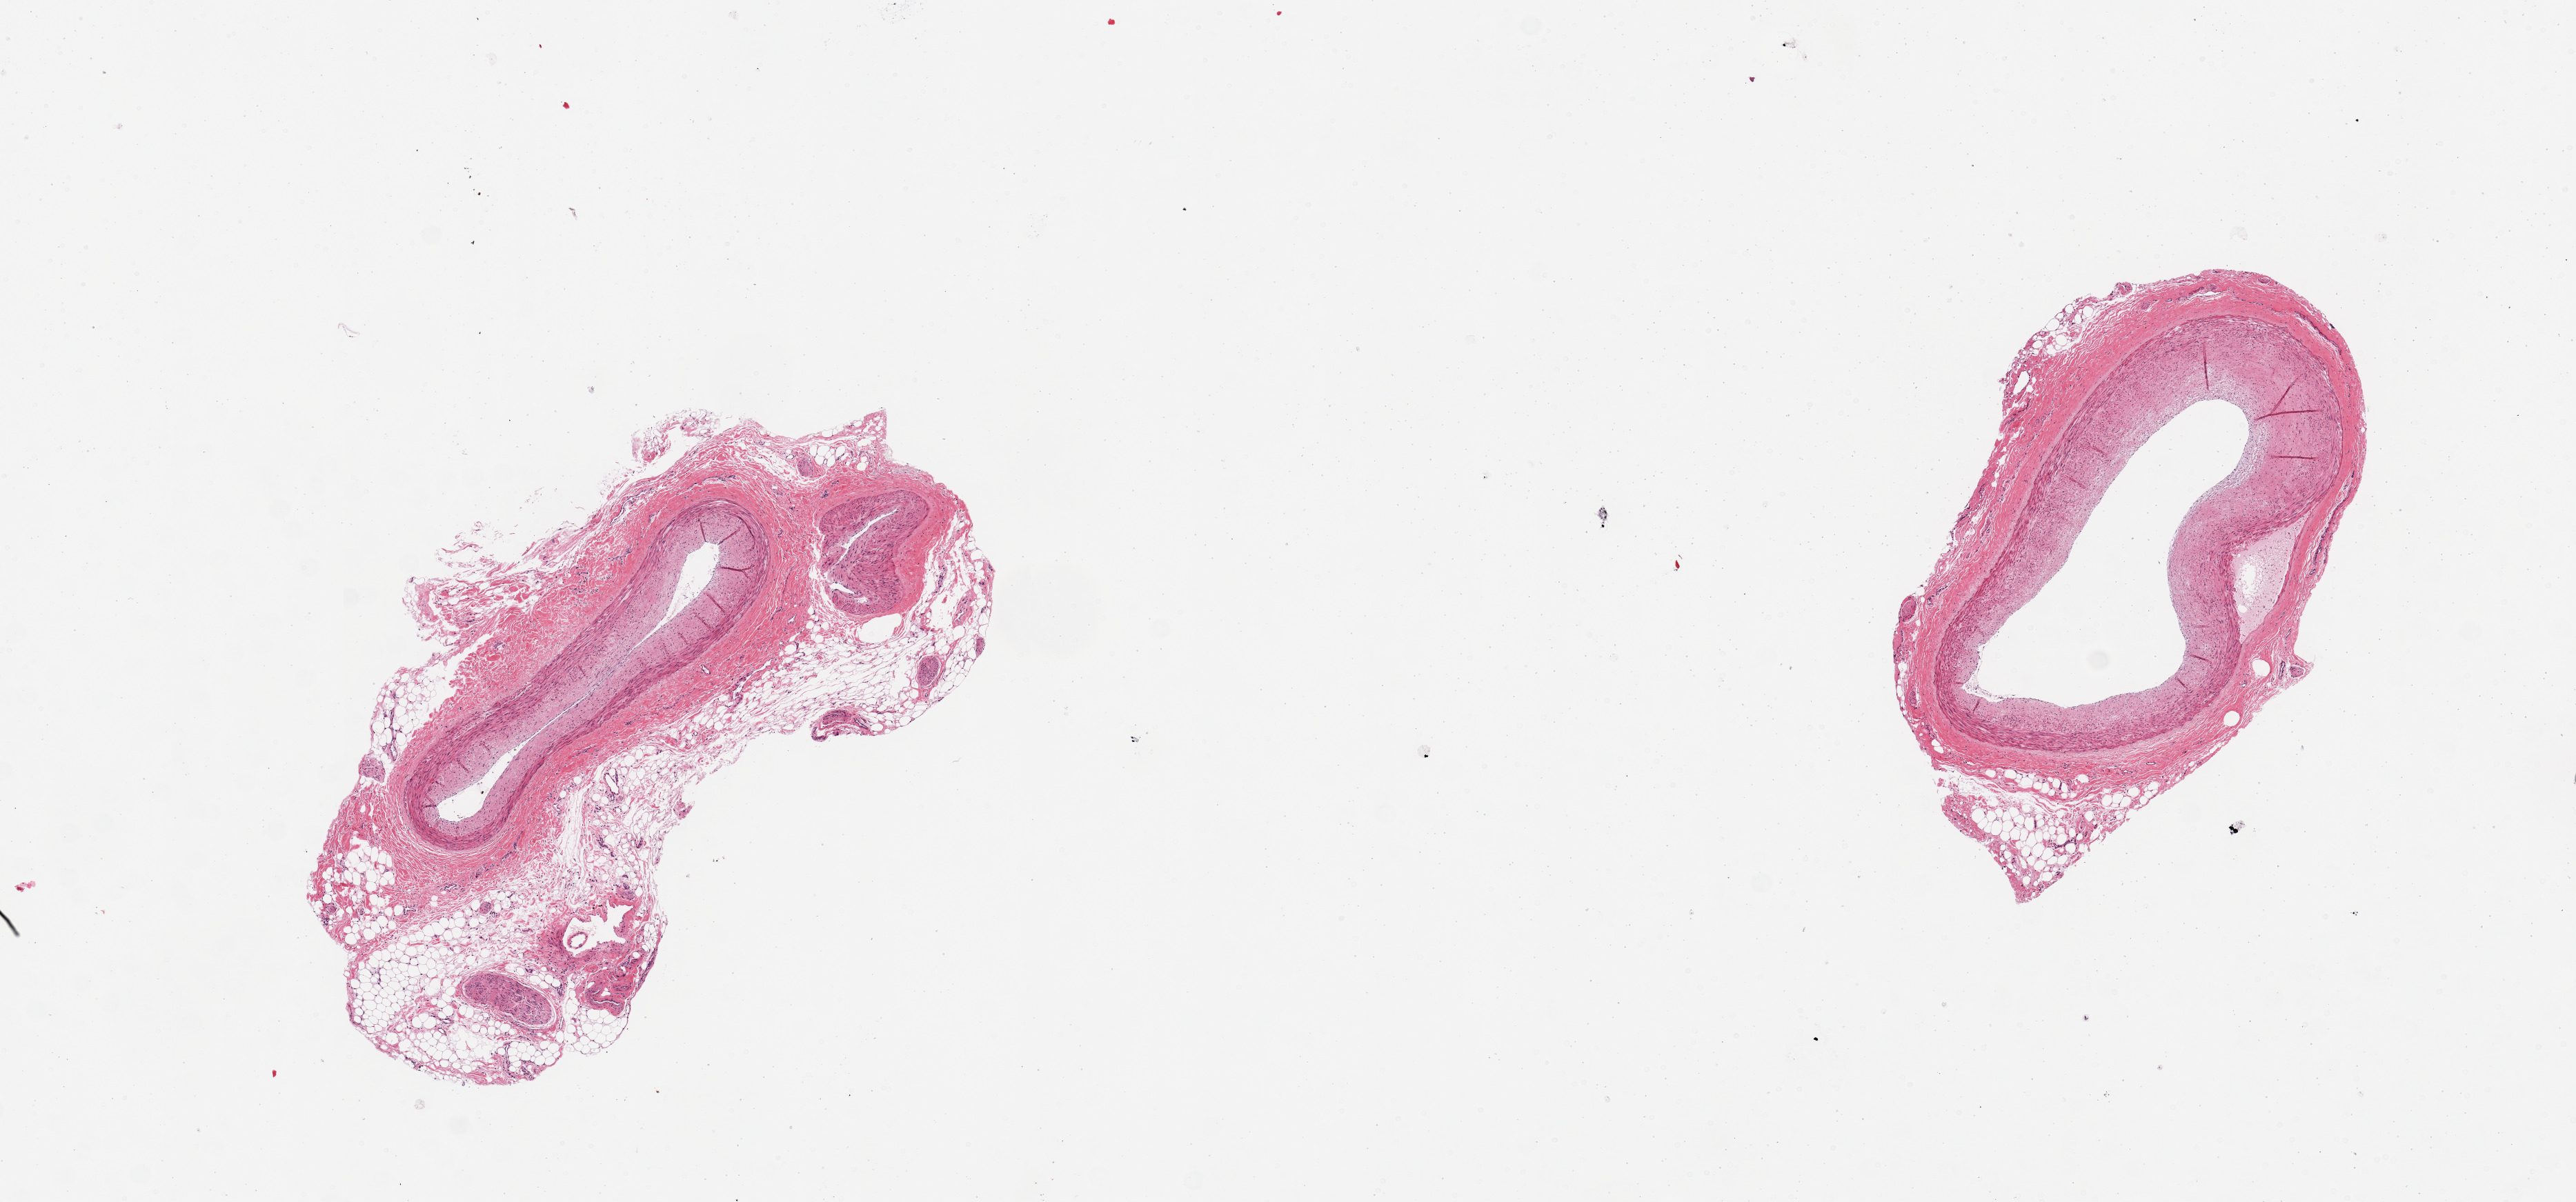
Digitized hematoxylin and eosin (H&E)-stained section, brightfield — low-resolution overview of the scanned area, about 14.8 x 6.9 mm. PAXgene-fixed, paraffin-embedded tissue. Sampled site (target tissue): coronary artery. Tissue donor sample. Donor sex: female.
- pathologist's review note for this sample: 2 pieces, one piece with 1.4mm attachment of fat, vessels, and nerve tissue